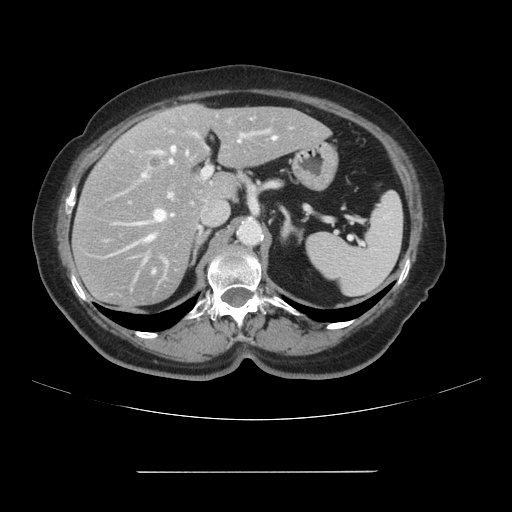
Contrast-enhanced abdominal CT, one axial slice; position 63 of 111 along the scan axis; 120 kVp; intravenous contrast given; soft-tissue window (W 400 / L 40 HU); 2.5 mm slice thickness; 512 × 512 image matrix, field of view 400 × 400 mm. Female patient, age 74 years. Case-level facts recorded for this patient, not image findings: diagnosis: colorectal cancer liver metastases, imaged before liver resection; multiple liver metastases: yes; largest metastasis: 1.1 cm; disease in both lobes: yes.
Outlined on this slice (outlined manually by an expert reader):
- hepatic veins: box from (x=106, y=137) to (x=276, y=281) px
- liver: (x=74, y=105)–(x=329, y=309)
- planned liver remnant (the part of the liver to remain after resection): (x=147, y=105)–(x=329, y=199)
- portal vein (with intrahepatic branches): (x=140, y=116)–(x=318, y=199)
- liver metastasis: (x=151, y=158)–(x=159, y=165)